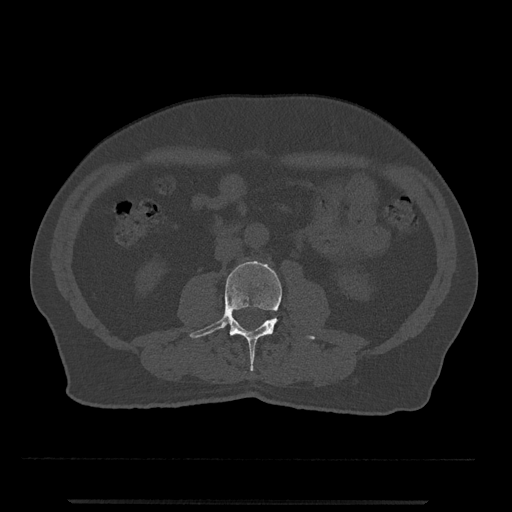
CT including the spine, one axial slice; slice 200 of 797 in the series (ordered by position); 120 kVp; bone window (W 1800 / L 400 HU); 0.5 mm slice thickness; 512 × 512 image matrix, field of view 419 × 419 mm. Patient: male, 63 years. From the clinical record (not read from this slice): primary cancer: prostate.
Outlined on this slice (semi-automatic segmentation, software-assisted and operator-edited):
- L3 vertebra: box from (x=189, y=261) to (x=315, y=372) px